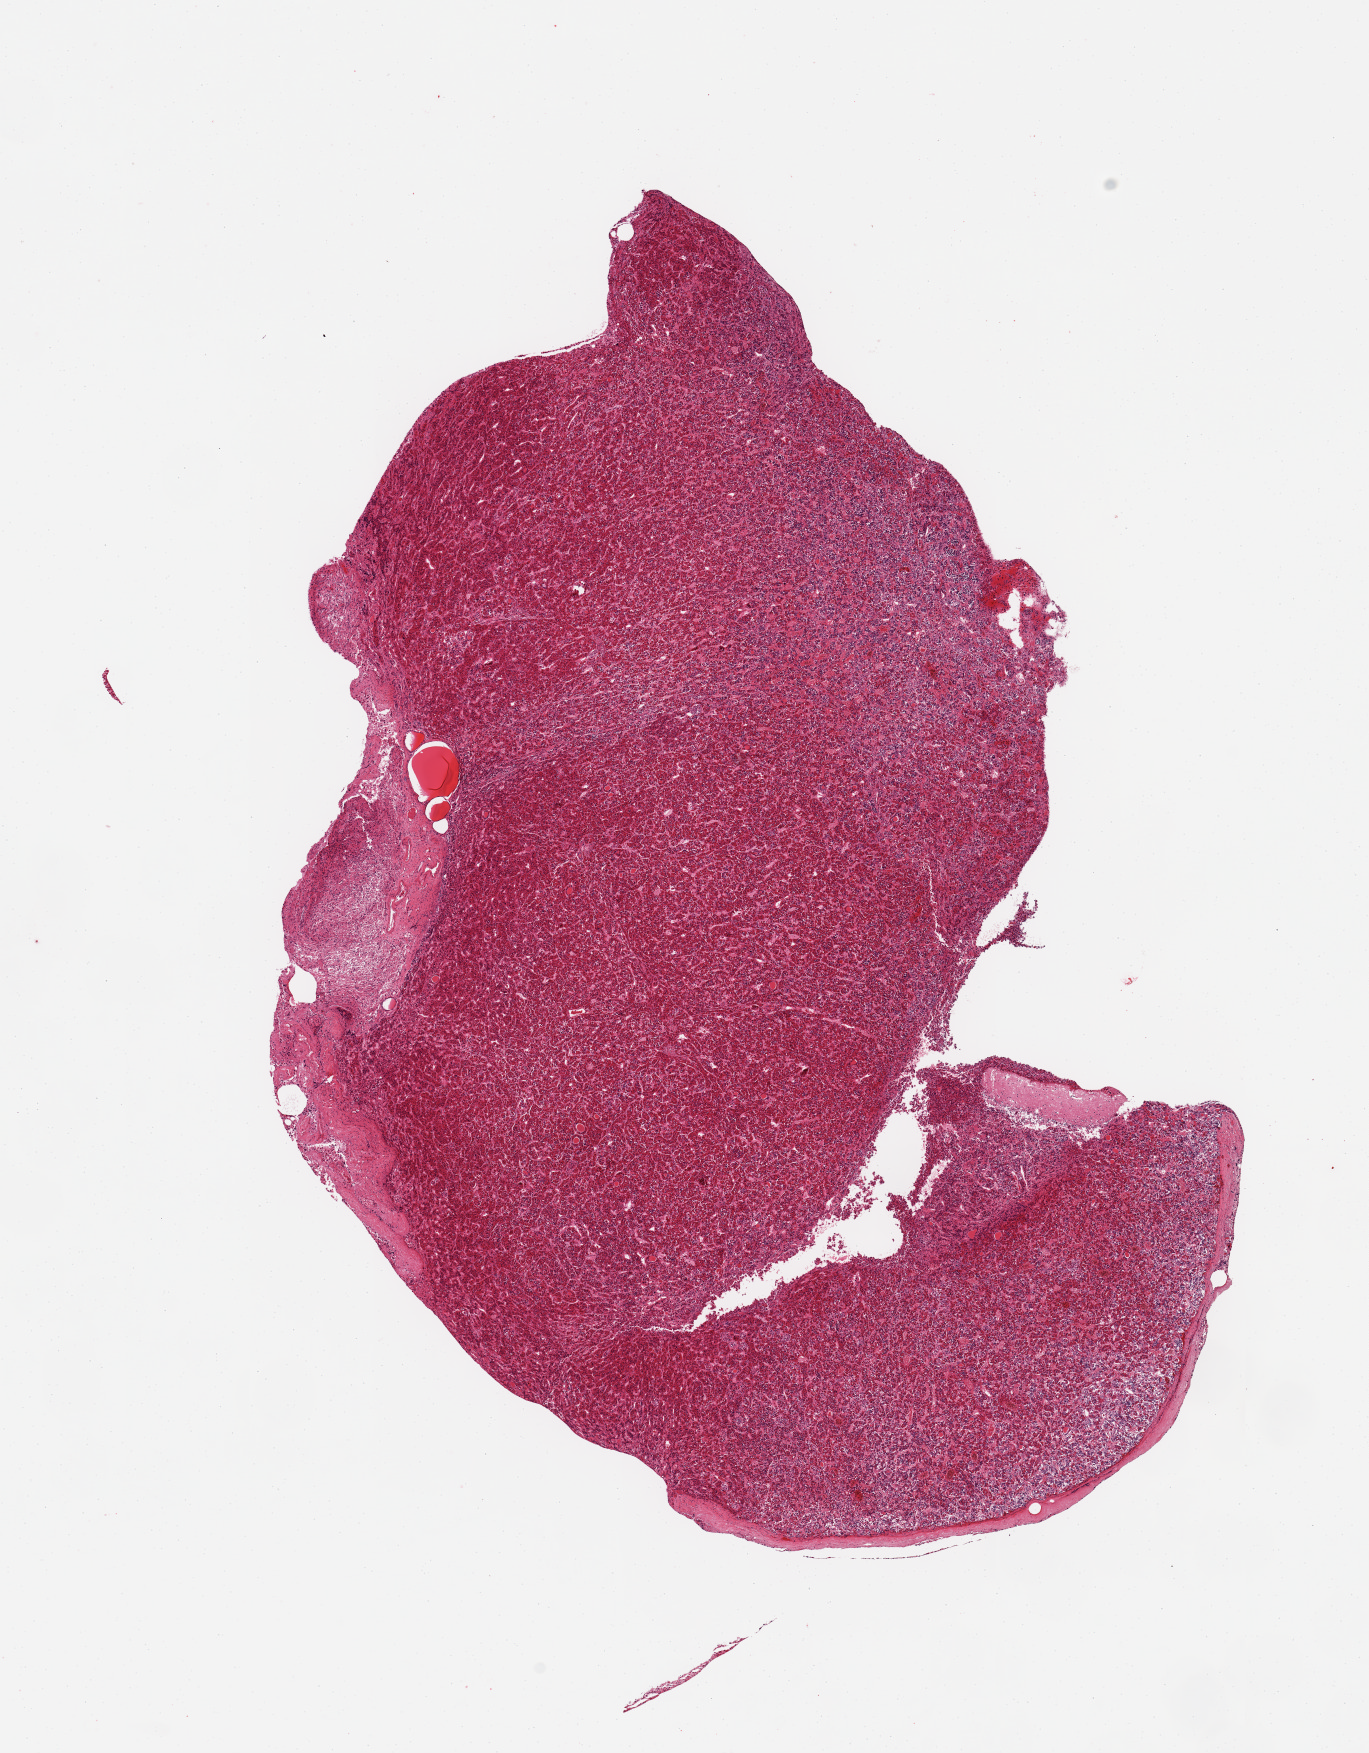
Whole-slide image, H&E stain, brightfield — shown as a low-resolution overview of the whole scanned area (about 10.8 x 13.9 mm). PAXgene-fixed paraffin-embedded (PFPE) section. Sampled site (target tissue): pituitary. Tissue donor sample. Donor: female.
Pathologist's review note for this sample: 1 piece; predominantly adenohypophysis with sparse neurohypophysis component.